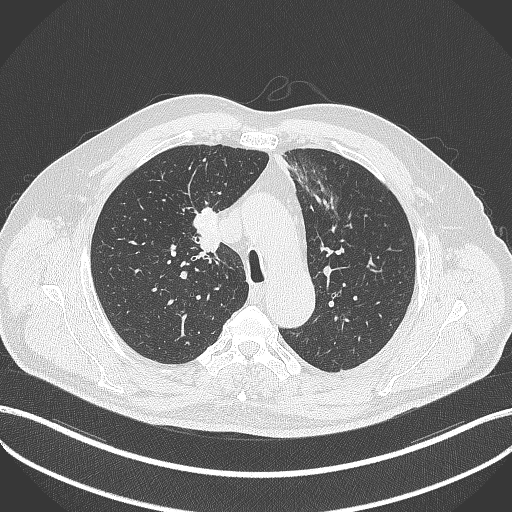
Chest CT, one axial slice. Position 280 of 411 along the scan axis. Lung window (W 1500 / L -600 HU). 1 mm slice thickness. 512 × 512 image matrix. Male patient, age 60 years. From the clinical record (not read from this slice): clinical TNM (as recorded): T1b N1 M0.
Structures marked on this image (bounding box drawn by a radiologist):
- lung tumour (recorded histology: squamous cell carcinoma): bounding box (x1, y1, x2, y2) in pixels: (192, 205, 223, 255)